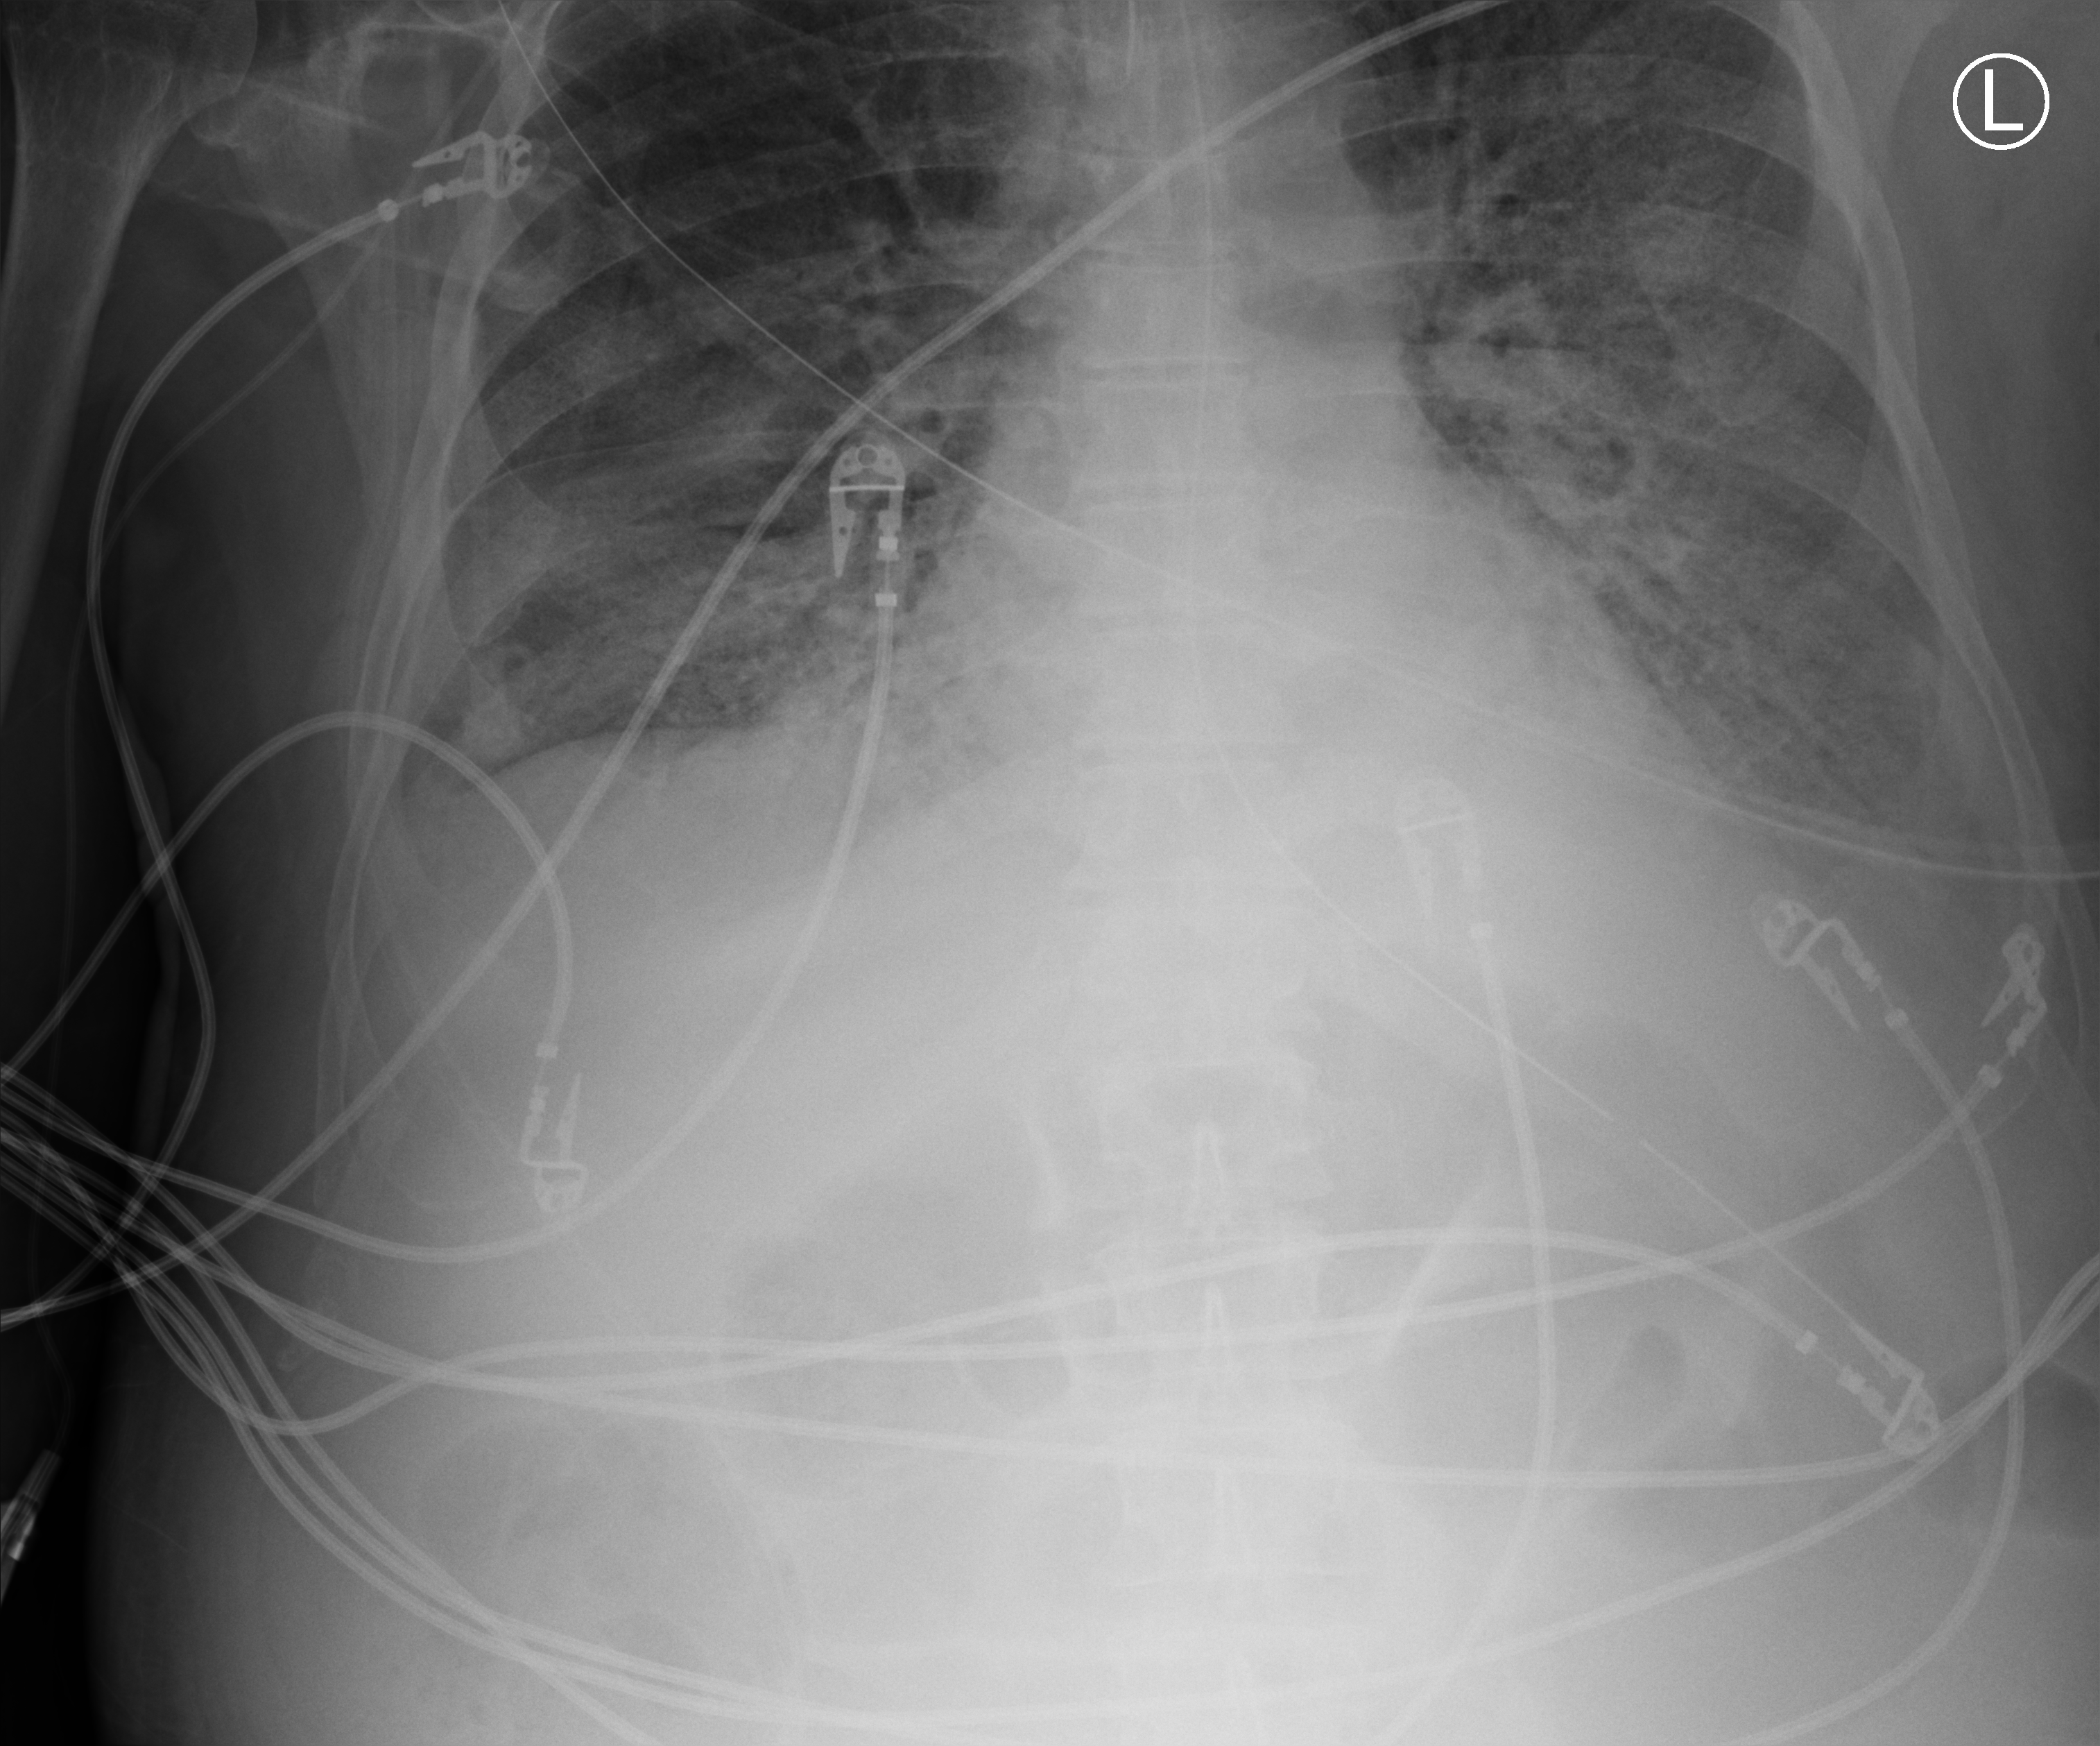
Bedside chest radiograph (computed radiography); anteroposterior (AP) projection. Patient hospitalised with COVID-19; male, aged 60–74 years.
From the hospital-stay record, not from the radiograph (when in the stay this image was taken is not recorded): hypertension (admission record): no; mechanically ventilated during this hospital stay: yes; admitted to intensive care during this hospital stay: yes.